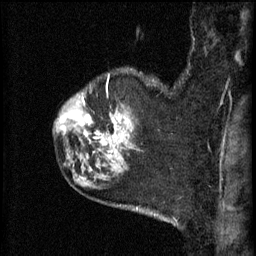
Breast MRI (dynamic contrast-enhanced), one sagittal slice; slice 50 of 60 in the series (ordered by position); 3 images stored at this slice position (order not interpretable as contrast timing); 1.5 T; TE 4.2 ms, TR 11 ms; 2.3 mm slice thickness; 256 × 256 image matrix, field of view 180 × 180 mm. Patient: female, 52 years.
Structures marked on this image (semi-automatically segmented with operator editing):
- analysis volume of interest (the breast-tissue region the enhancement analysis was run in; not a lesion): bounding box [x1, y1, x2, y2] px = [86, 76, 142, 157]
- tumour enhancement mask (voxels above the 70 % enhancement threshold inside the analysis volume of interest): [98, 114, 116, 141]